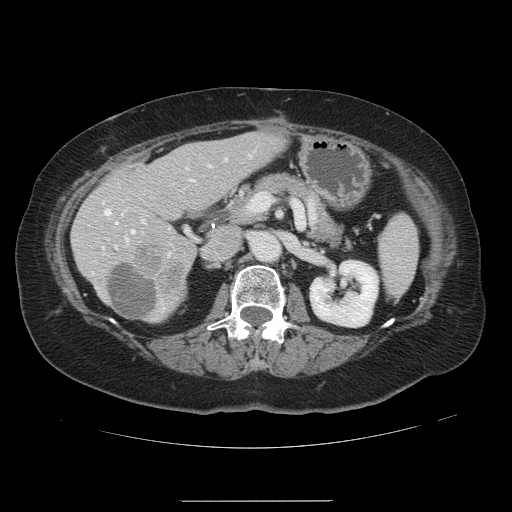
Contrast-enhanced abdominal CT, one axial slice; position 60 of 141 along the scan axis; 120 kVp; intravenous contrast given; soft-tissue window (W 400 / L 40 HU); 2.5 mm slice thickness; 512 × 512 image matrix, field of view 393 × 393 mm. Female patient, age 74 years. Case-level facts recorded for this patient, not image findings: diagnosis: colorectal cancer liver metastases, imaged before liver resection; multiple liver metastases: yes; largest metastasis: 7 cm; disease in both lobes: yes.
Structures marked on this image (outlined manually by an expert reader):
- hepatic veins: bounding box <105,209,134,241> (left, top, right, bottom; pixels)
- liver: <72,133,285,323>
- planned liver remnant (the part of the liver to remain after resection): <74,133,285,319>
- portal vein (with intrahepatic branches): <115,157,226,256>
- liver metastasis: <109,263,158,320>
- liver metastasis: <131,243,184,294>